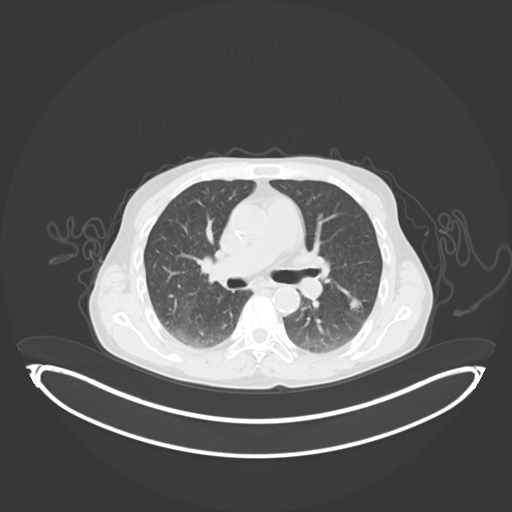
Chest CT, one axial slice. Position 58 of 102 along the scan axis. Reconstruction kernel B30f. Lung window (W 1500 / L -600 HU). 3 mm slice thickness. 512 × 512 image matrix, field of view 500 × 500 mm. Patient: male, 58 years. Case-level facts recorded for this patient, not image findings: clinical TNM (as recorded): T1c N0 M0.
Annotated regions visible in this slice (bounding box drawn by a radiologist):
- lung tumour (recorded histology: adenocarcinoma): bounding box (x1, y1, x2, y2) in pixels: (348, 295, 365, 314)